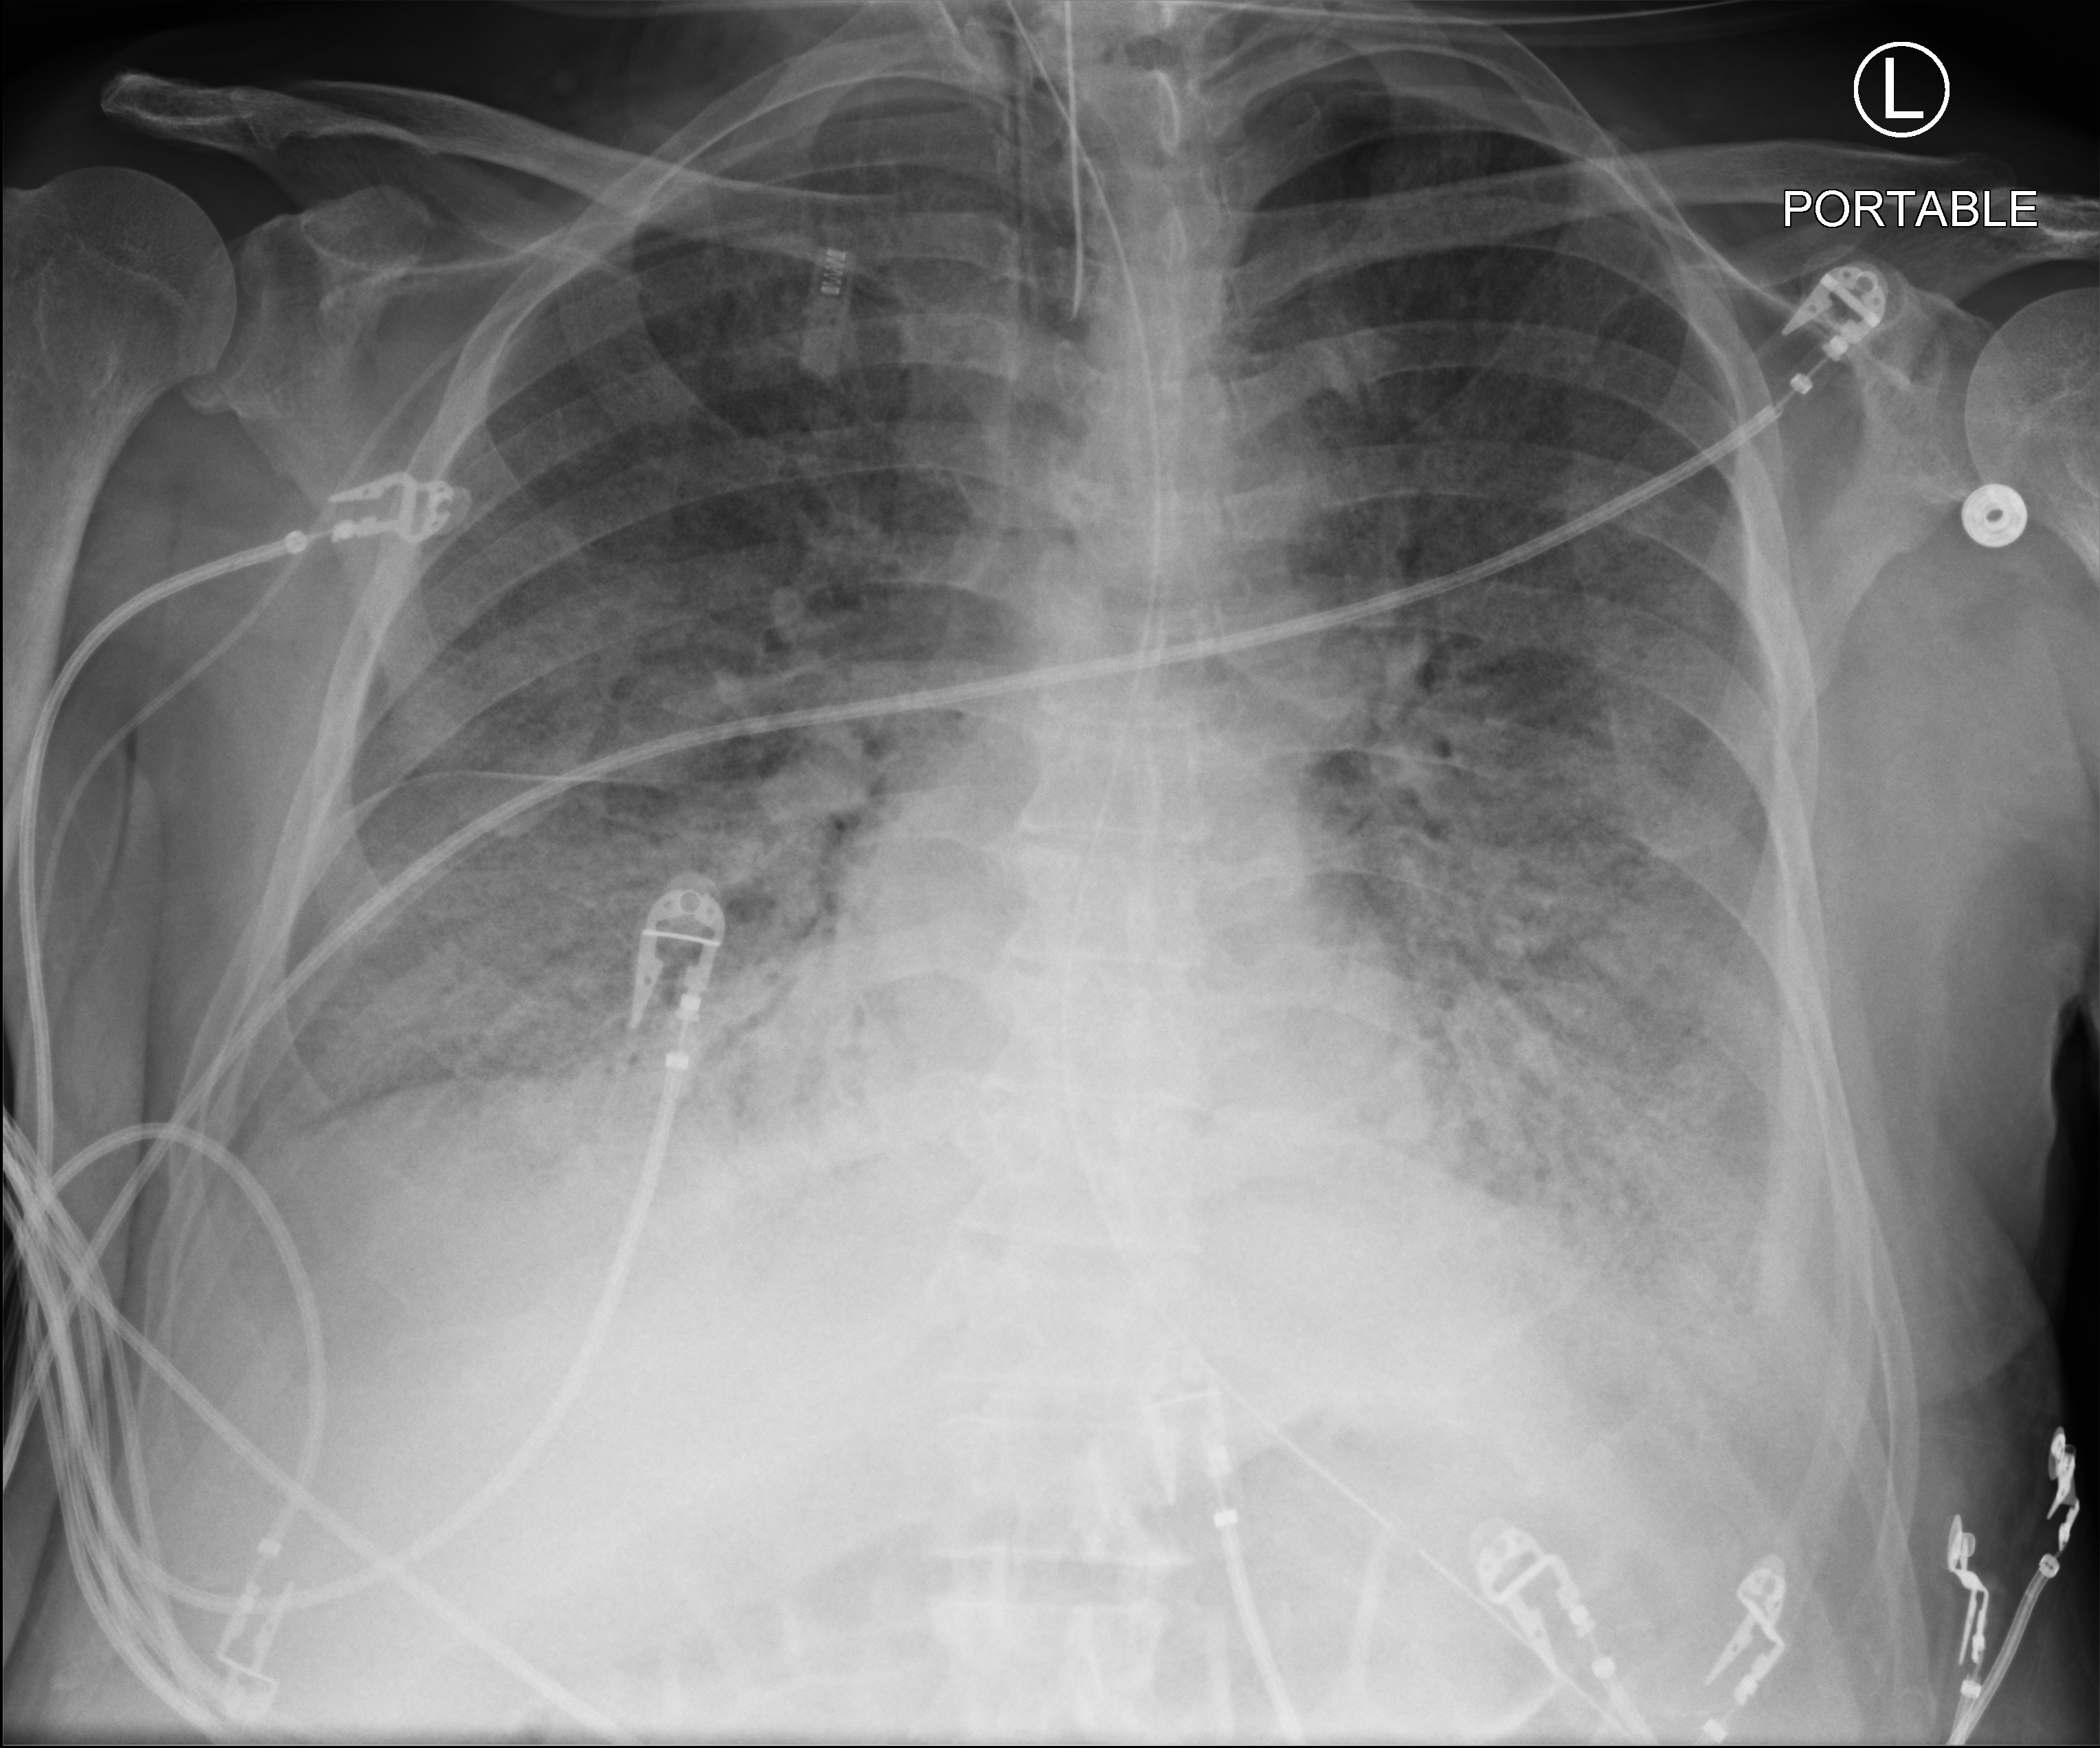
Bedside chest radiograph (computed radiography). Male patient hospitalised with COVID-19, age 60–74 years.
Admission-level facts for this patient (not findings on this image; timing relative to this image not recorded): length of hospital stay: 24 days.